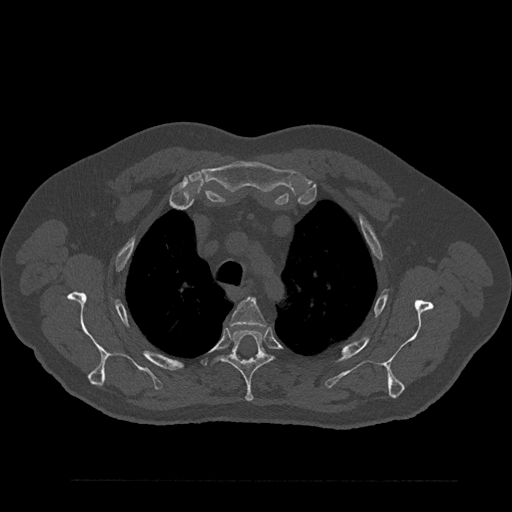
CT including the spine, one axial slice; slice 651 of 797 in the series (ordered by position); reconstruction kernel Br40s/3; 120 kVp; bone window (W 1800 / L 400 HU); 0.5 mm slice thickness; 512 × 512 image matrix, field of view 430 × 430 mm. Patient: male, 61 years. Case-level facts recorded for this patient, not image findings: primary cancer: prostate.
Outlined on this slice (semi-automatically segmented with operator editing):
- T3 vertebra: bounding box <230,298,266,327> (left, top, right, bottom; pixels)
- T4 vertebra: <221,329,272,401>